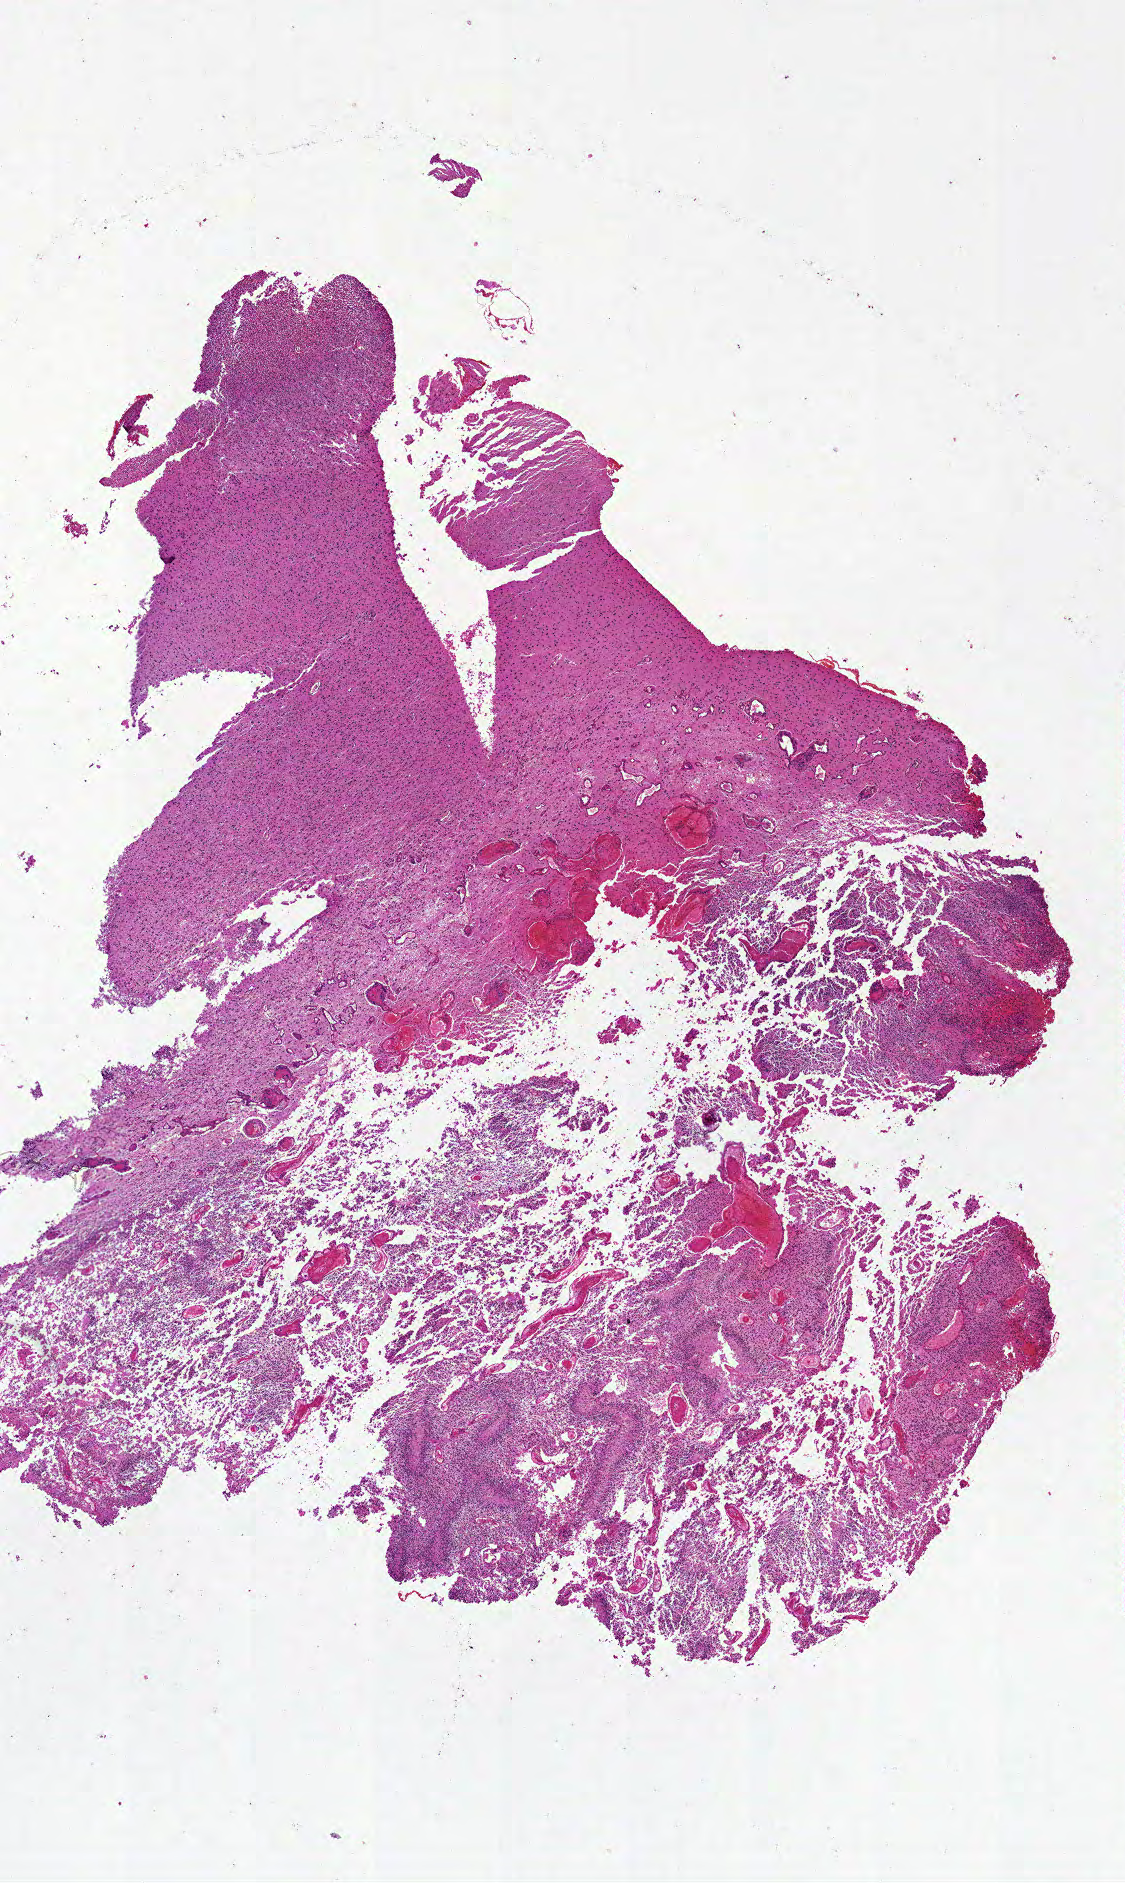
H&E whole-slide image — a low-resolution overview of the entire scanned area, about 9.0 x 15.0 mm (acquisition: 20x scan). FFPE section. Brain, primary tumour sample. Patient: female, age at initial diagnosis 49 years.
Diagnosis: Glioblastoma.